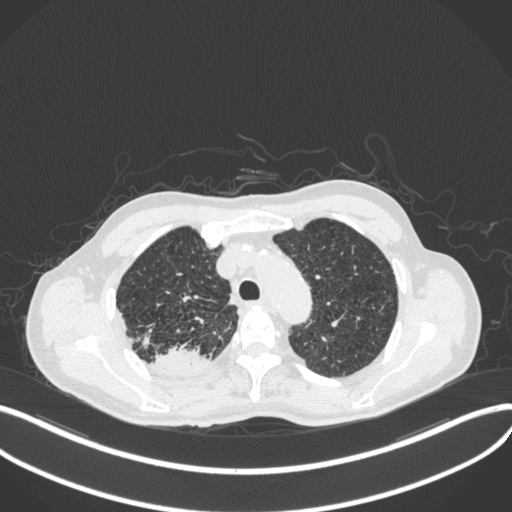
Chest CT, one axial slice. Position 344 of 423 along the scan axis. 120 kVp. Lung window (W 1500 / L -600 HU). 1 mm slice thickness. 512 × 512 image matrix, field of view 400 × 400 mm. Patient: male, 79 years. From the clinical record (not read from this slice): clinical TNM (as recorded): T3 N0 M0.
Annotated regions visible in this slice (rectangle marked by the reading radiologist):
- lung tumour (recorded histology: adenocarcinoma): bounding box <153,344,205,371> (left, top, right, bottom; pixels)